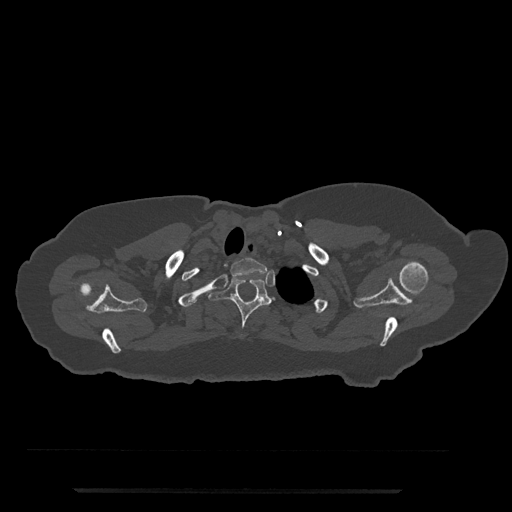
CT including the spine, one axial slice. Slice 680 of 797 in the series (ordered by position). Reconstruction kernel Br40s/3. 120 kVp. Bone window (W 1800 / L 400 HU). 0.5 mm slice thickness. 512 × 512 image matrix, field of view 440 × 440 mm. Patient: female, 51 years. Case-level facts recorded for this patient, not image findings: primary cancer: neuro; vertebrae with lytic lesions (as recorded): T8.
Annotated regions visible in this slice (semi-automatic segmentation, software-assisted and operator-edited):
- T1 vertebra: bounding box [x1, y1, x2, y2] px = [230, 257, 267, 275]
- T2 vertebra: [209, 277, 271, 337]